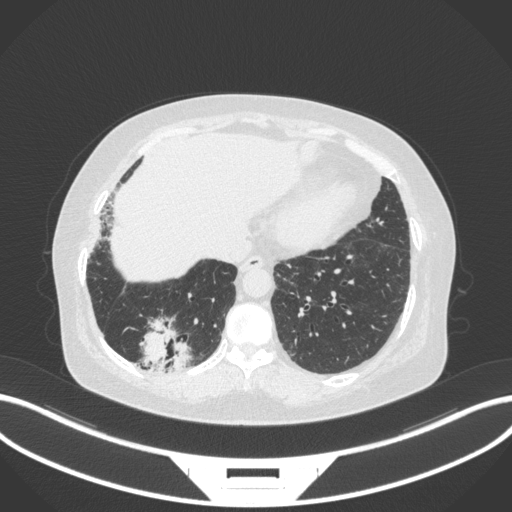
Chest CT, one axial slice. Slice 43 of 303 in the series (ordered by position). Reconstruction kernel B31f. 120 kVp. Lung window (W 1500 / L -600 HU). 1 mm slice thickness. 512 × 512 image matrix. Female patient, age 65 years. Case-level facts recorded for this patient, not image findings: clinical TNM (as recorded): T2b N1 M0.
Annotated regions visible in this slice (rectangle marked by the reading radiologist):
- lung tumour (recorded histology: adenocarcinoma): bounding box (x1, y1, x2, y2) in pixels: (138, 313, 193, 374)